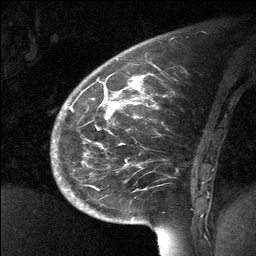
Breast MRI (dynamic contrast-enhanced), one sagittal slice. Slice 20 of 64 in the series (ordered by position). Dynamic contrast-enhanced study with each time point stored as its own series, time point 2 of 3 at this slice position (early post-contrast, ordered by acquisition time). 1.5 T. TE 4.8 ms, TR 27 ms. 2 mm slice thickness. 256 × 256 image matrix, field of view 200 × 200 mm. Female patient, age 39 years. Case-level facts recorded for this patient, not image findings: setting: breast cancer imaged before/during neoadjuvant chemotherapy; receptor status: HER2-positive.
Annotated regions visible in this slice (semi-automatic segmentation, software-assisted and operator-edited):
- analysis volume of interest (the breast-tissue region the enhancement analysis was run in; not a lesion): bounding box <70,69,202,224> (left, top, right, bottom; pixels)
- tumour enhancement mask (voxels above the 90 % enhancement threshold inside the analysis volume of interest): <107,77,140,117>